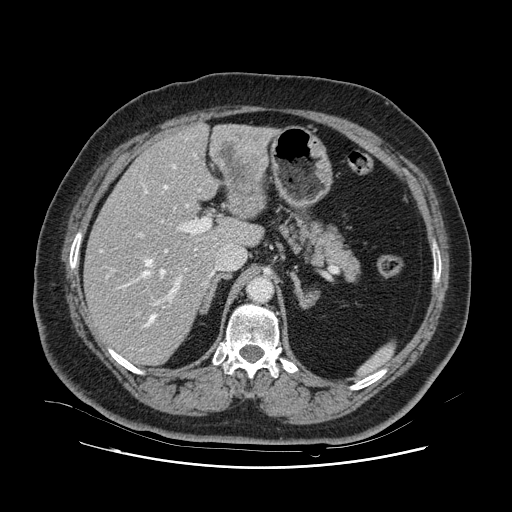
Contrast-enhanced abdominal CT, one axial slice. Position 69 of 132 along the scan axis. Soft-tissue window (W 400 / L 40 HU). 2.5 mm slice thickness. 512 × 512 image matrix, field of view 391 × 391 mm. Female patient, age 73 years. From the clinical record (not read from this slice): diagnosis: colorectal cancer liver metastases, imaged before liver resection; multiple liver metastases: no; largest metastasis: 7 cm; disease in both lobes: no.
Outlined on this slice (manually delineated by an expert):
- hepatic veins: bounding box [x1, y1, x2, y2] px = [100, 165, 221, 327]
- liver: [85, 124, 271, 365]
- planned liver remnant (the part of the liver to remain after resection): [85, 153, 243, 365]
- portal vein (with intrahepatic branches): [112, 184, 211, 306]
- liver metastasis: [220, 142, 256, 199]